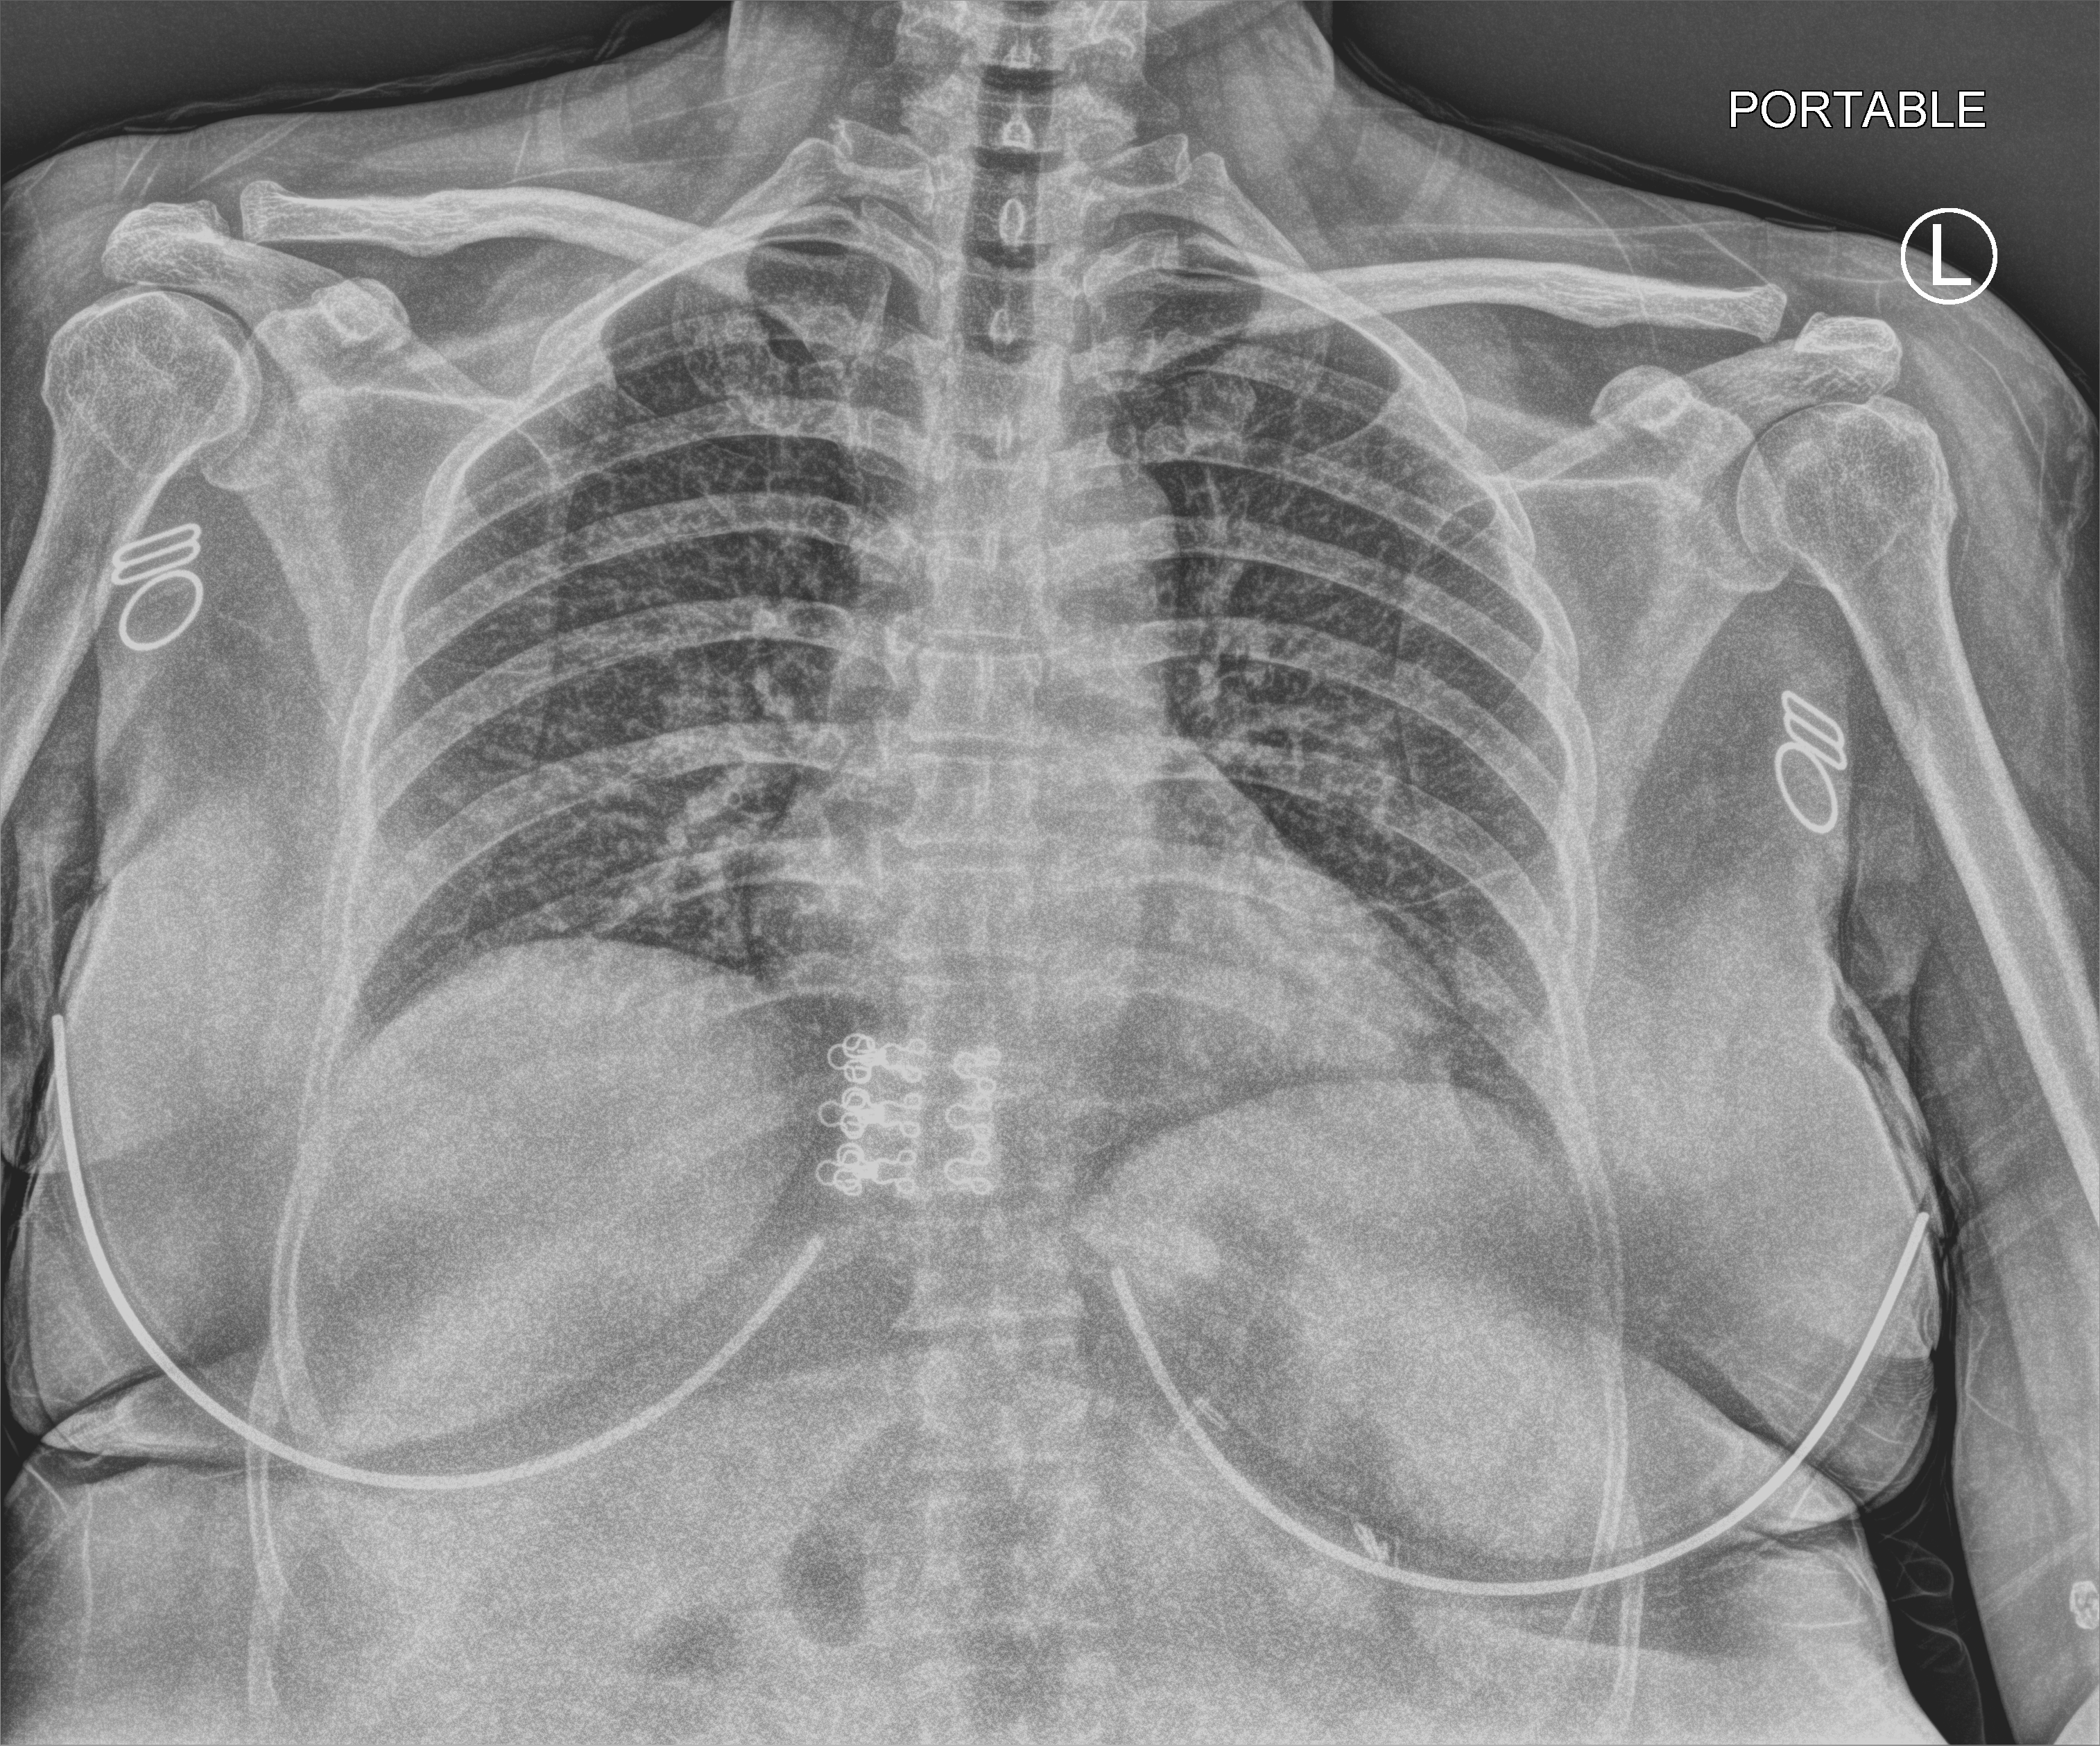
Bedside chest radiograph (computed radiography); anteroposterior (AP) projection. Patient hospitalised with COVID-19; female, aged 18–59 years.
From the hospital-stay record, not from the radiograph (when in the stay this image was taken is not recorded): chronic kidney disease (admission record): yes; admitted to intensive care during this hospital stay: no; other chronic lung disease (admission record): no.